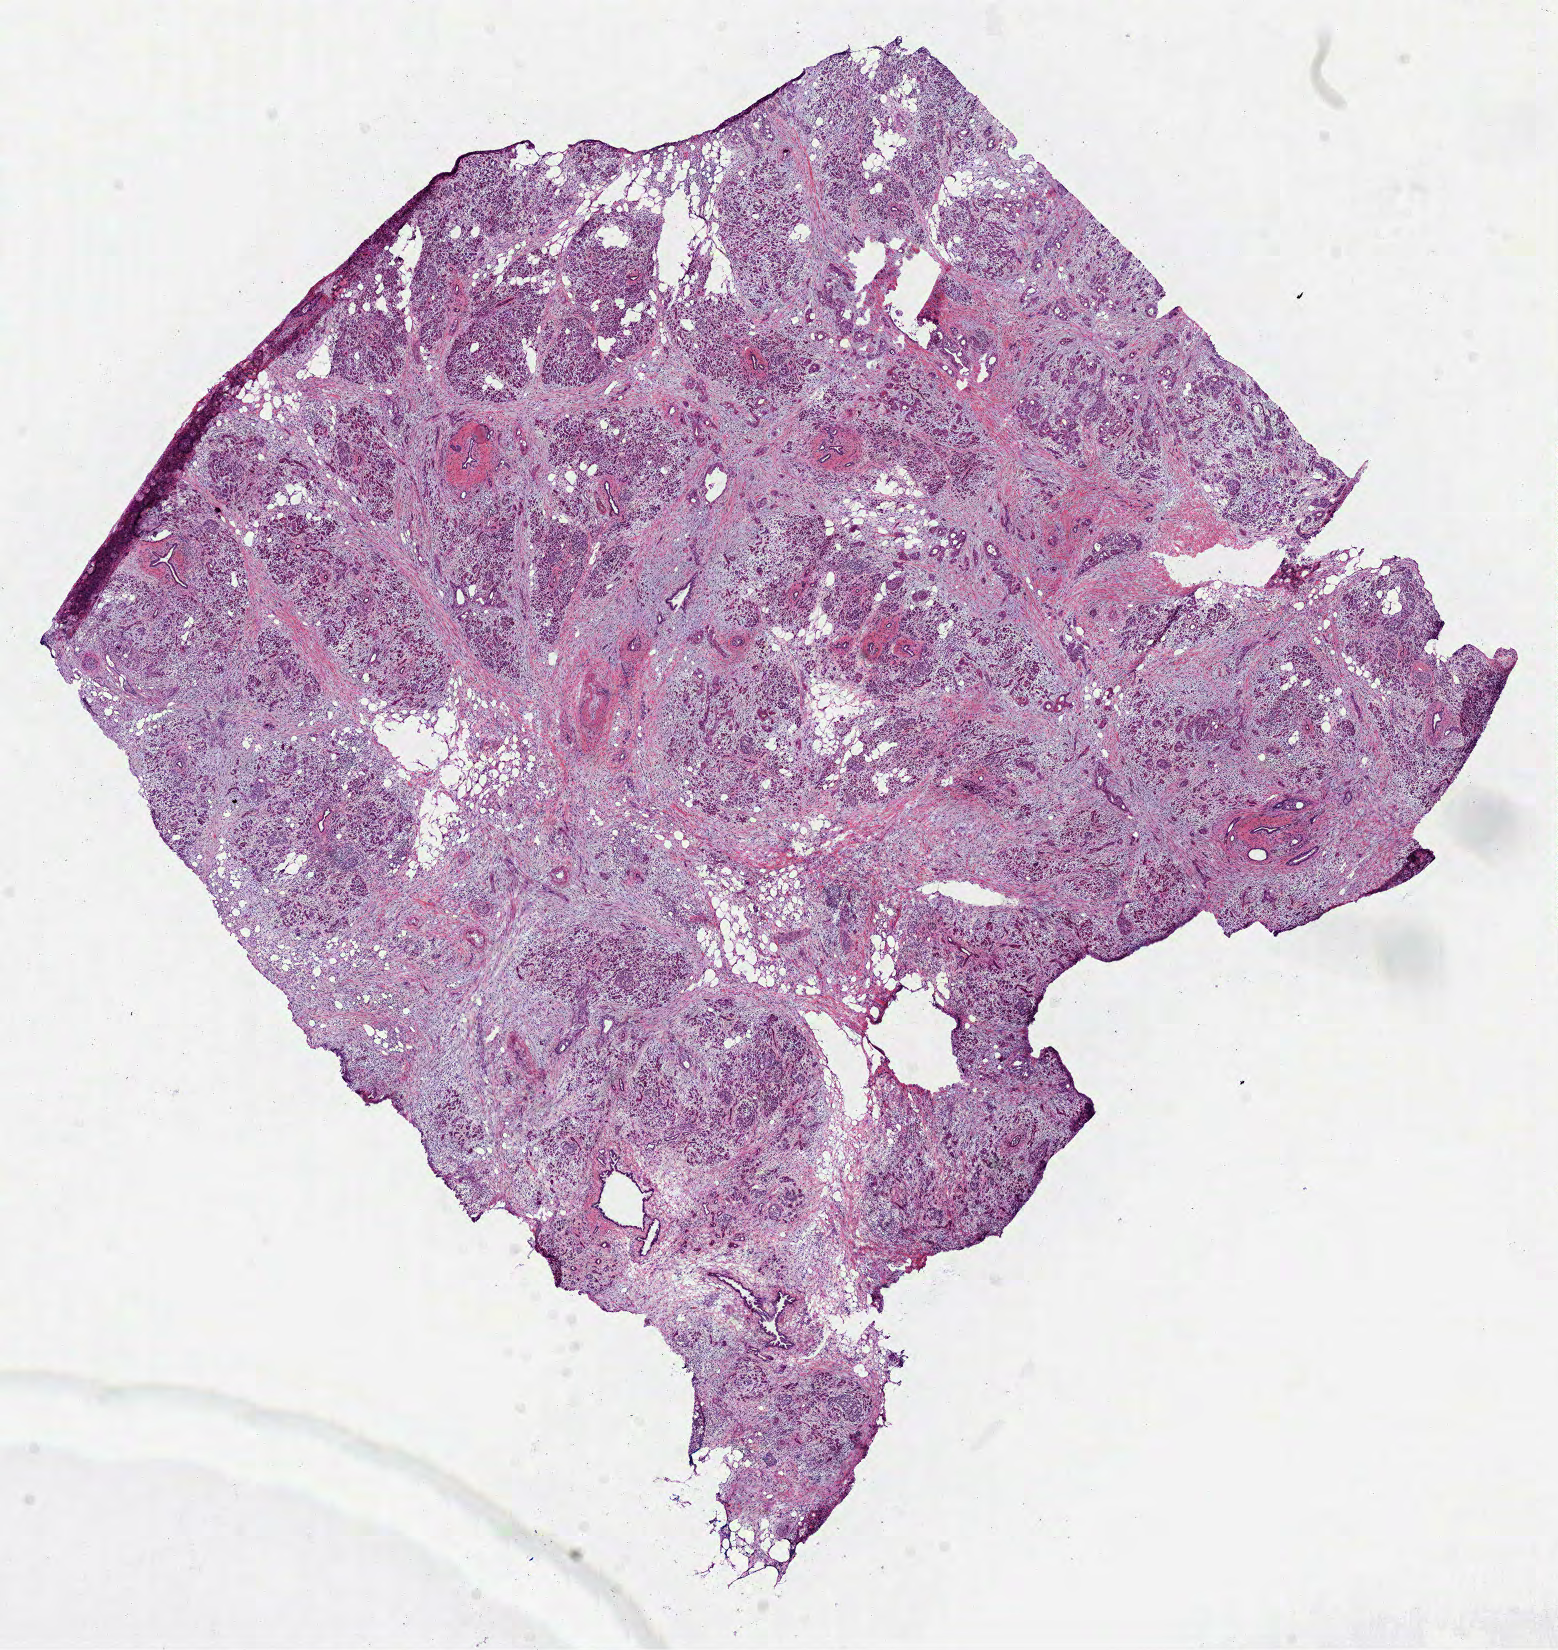
H&E-stained whole-slide image — a low-resolution overview of the entire scanned area, about 12.6 x 13.3 mm (slide scanned at 40x). Frozen section. Sample: primary tumour, pancreas. Male patient; age at initial diagnosis 61 years. Histologic grade: G2 (moderately differentiated). Slide review estimates, as recorded: tumour cells 10%, tumour nuclei 10%, normal cells 90%, stromal cells 0%, necrosis 0%.
Lymph nodes positive (case pathology): 4 of 33 examined. AJCC pathologic stage: IIB (7th edition). TNM: T3 N1 MX. Pathologic diagnosis: Infiltrating duct carcinoma, NOS (head of pancreas).